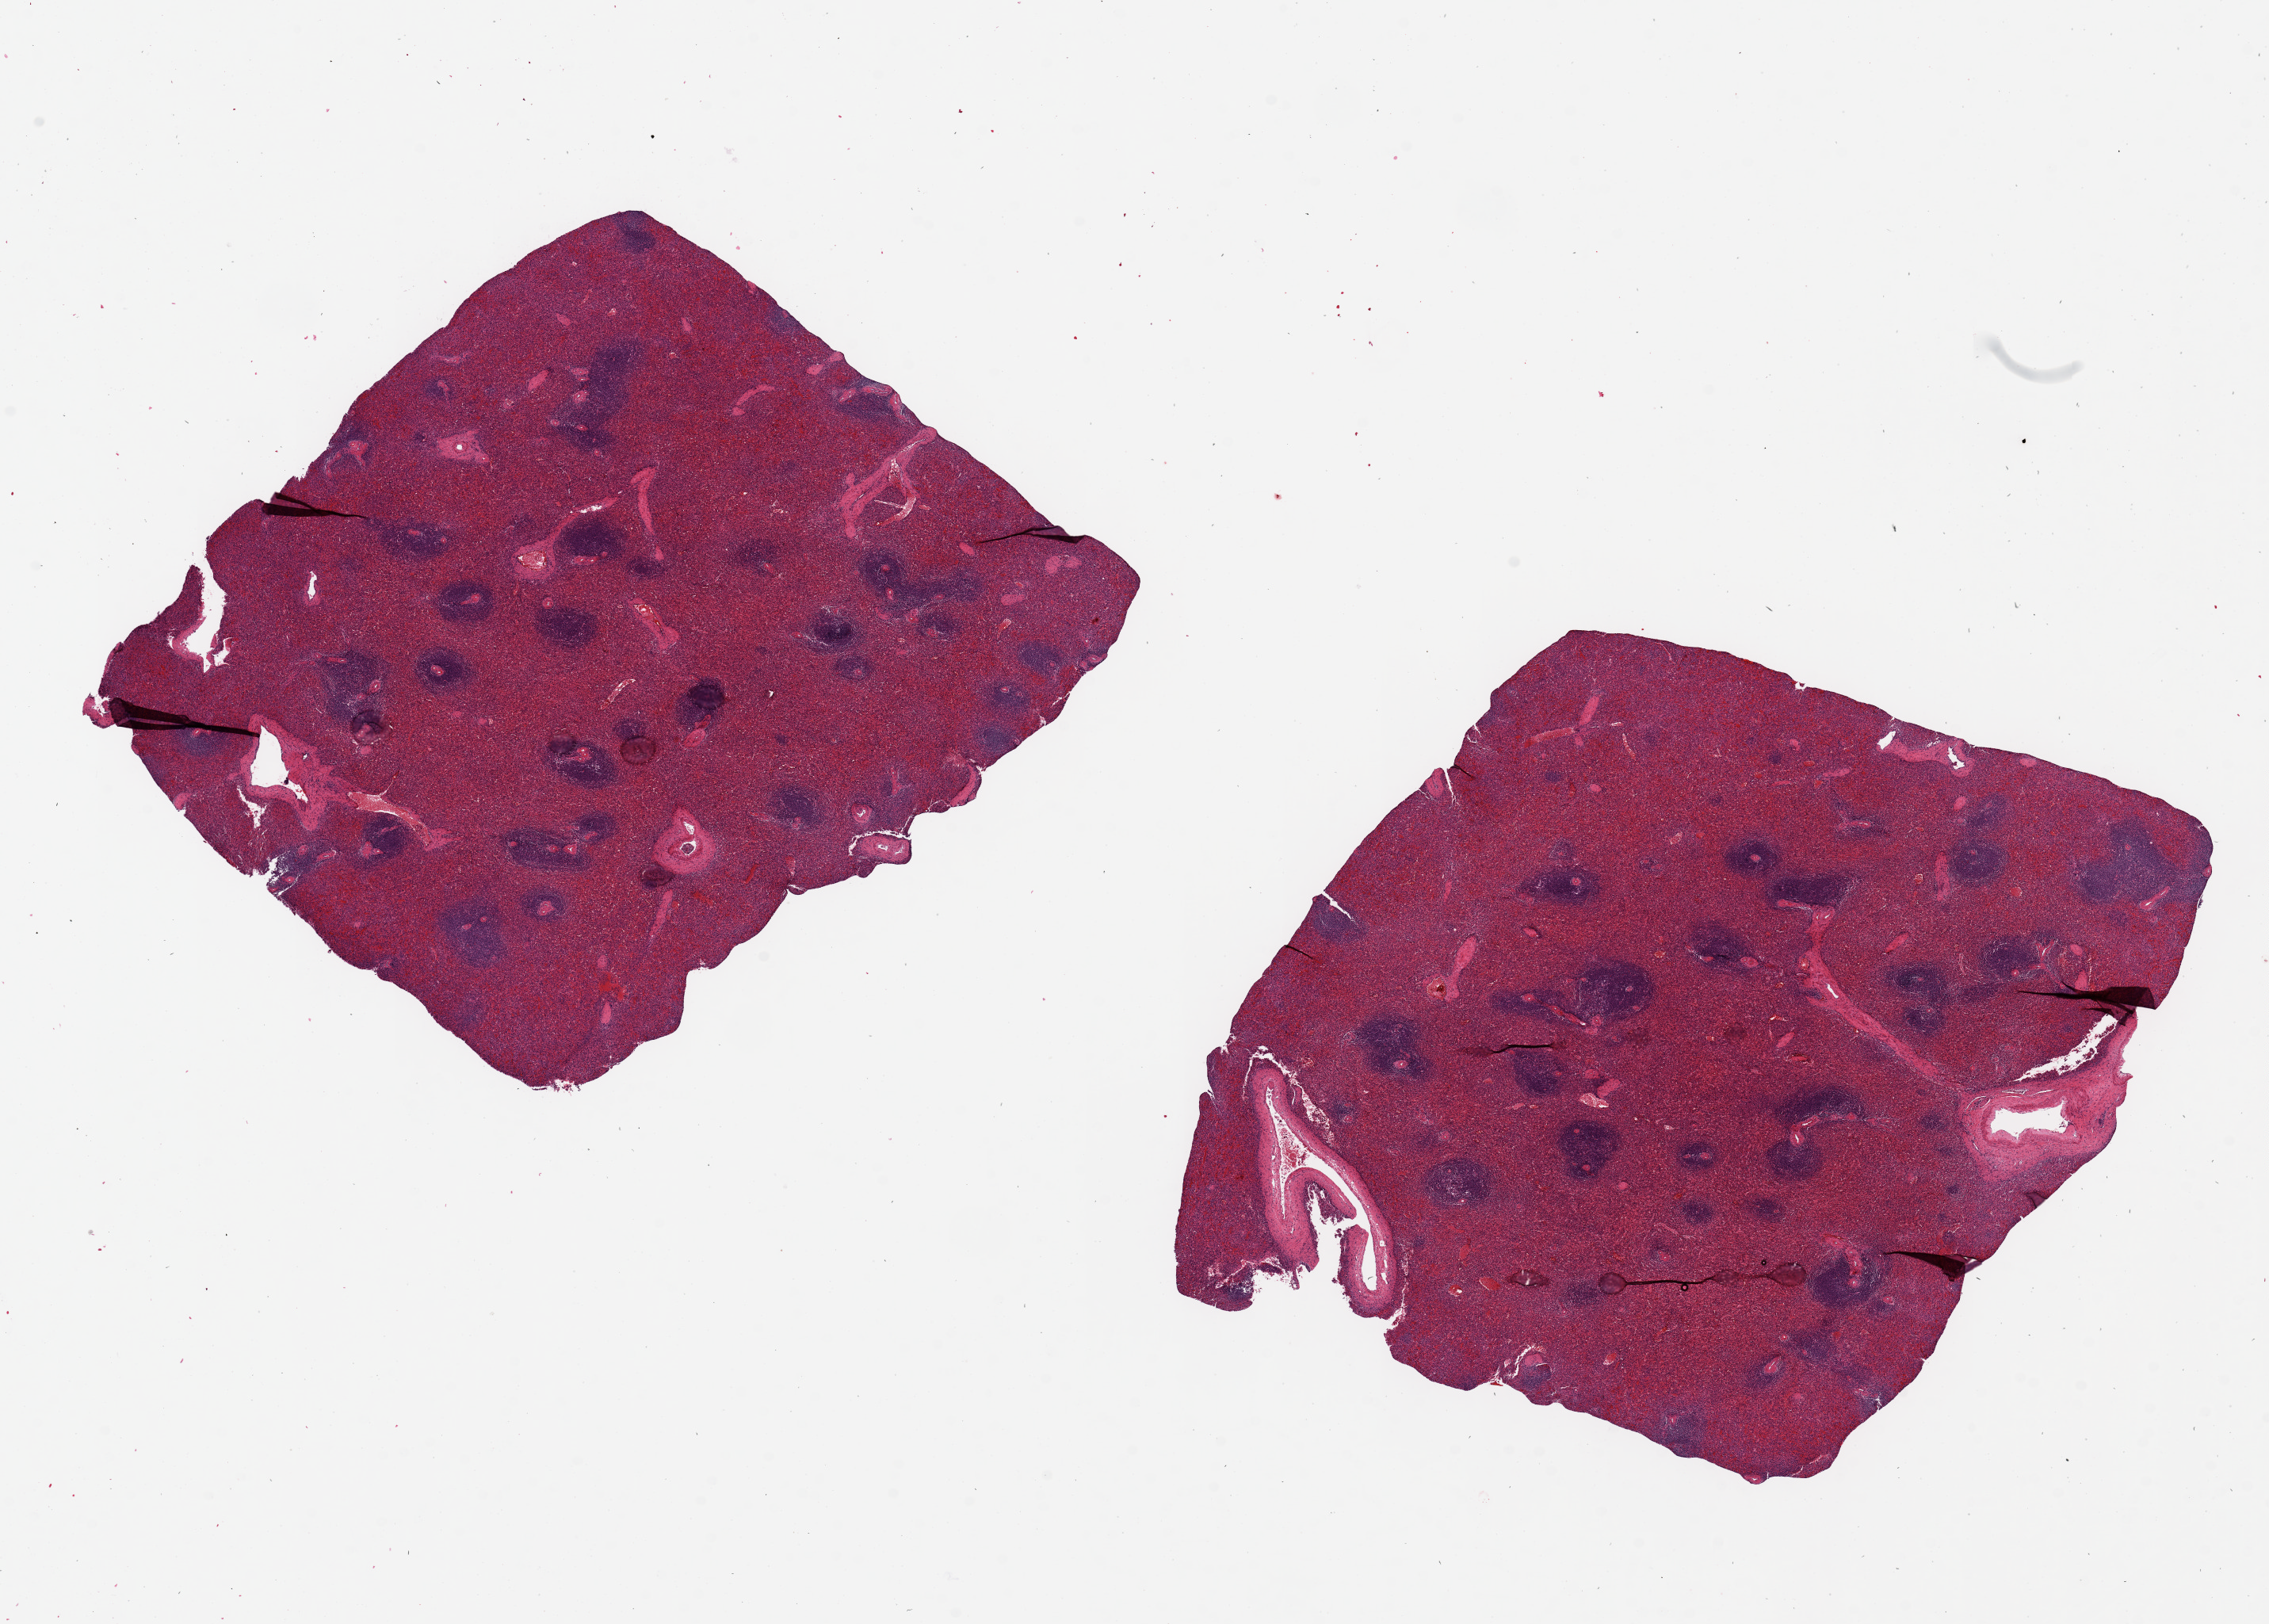
H&E whole-slide image, whole scanned area (about 22.6 x 16.2 mm) shown as a low-resolution overview, PAXgene-fixed, paraffin-embedded tissue, section of spleen (target tissue), tissue donor sample. Donor sex: female.
• review note (as recorded): 2 pieces, 8x7 & 8x7mm; moderate congestion; discrete small lymphoid nodules